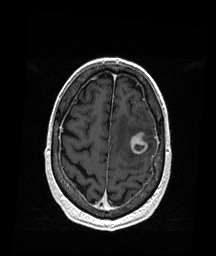
Brain MRI from a brain-tumour surgery series, one axial slice. Slice 47 of 176 in the series (ordered by position). T1-weighted post-contrast. 1 mm slice thickness. 216 × 256 image matrix. From the clinical record (not read from this slice): histopathology: Metastatic Melanoma; tumour location: Left Frontal.
Structures marked on this image (manually delineated by an expert):
- tumour: bounding box <129,131,148,154> (left, top, right, bottom; pixels)